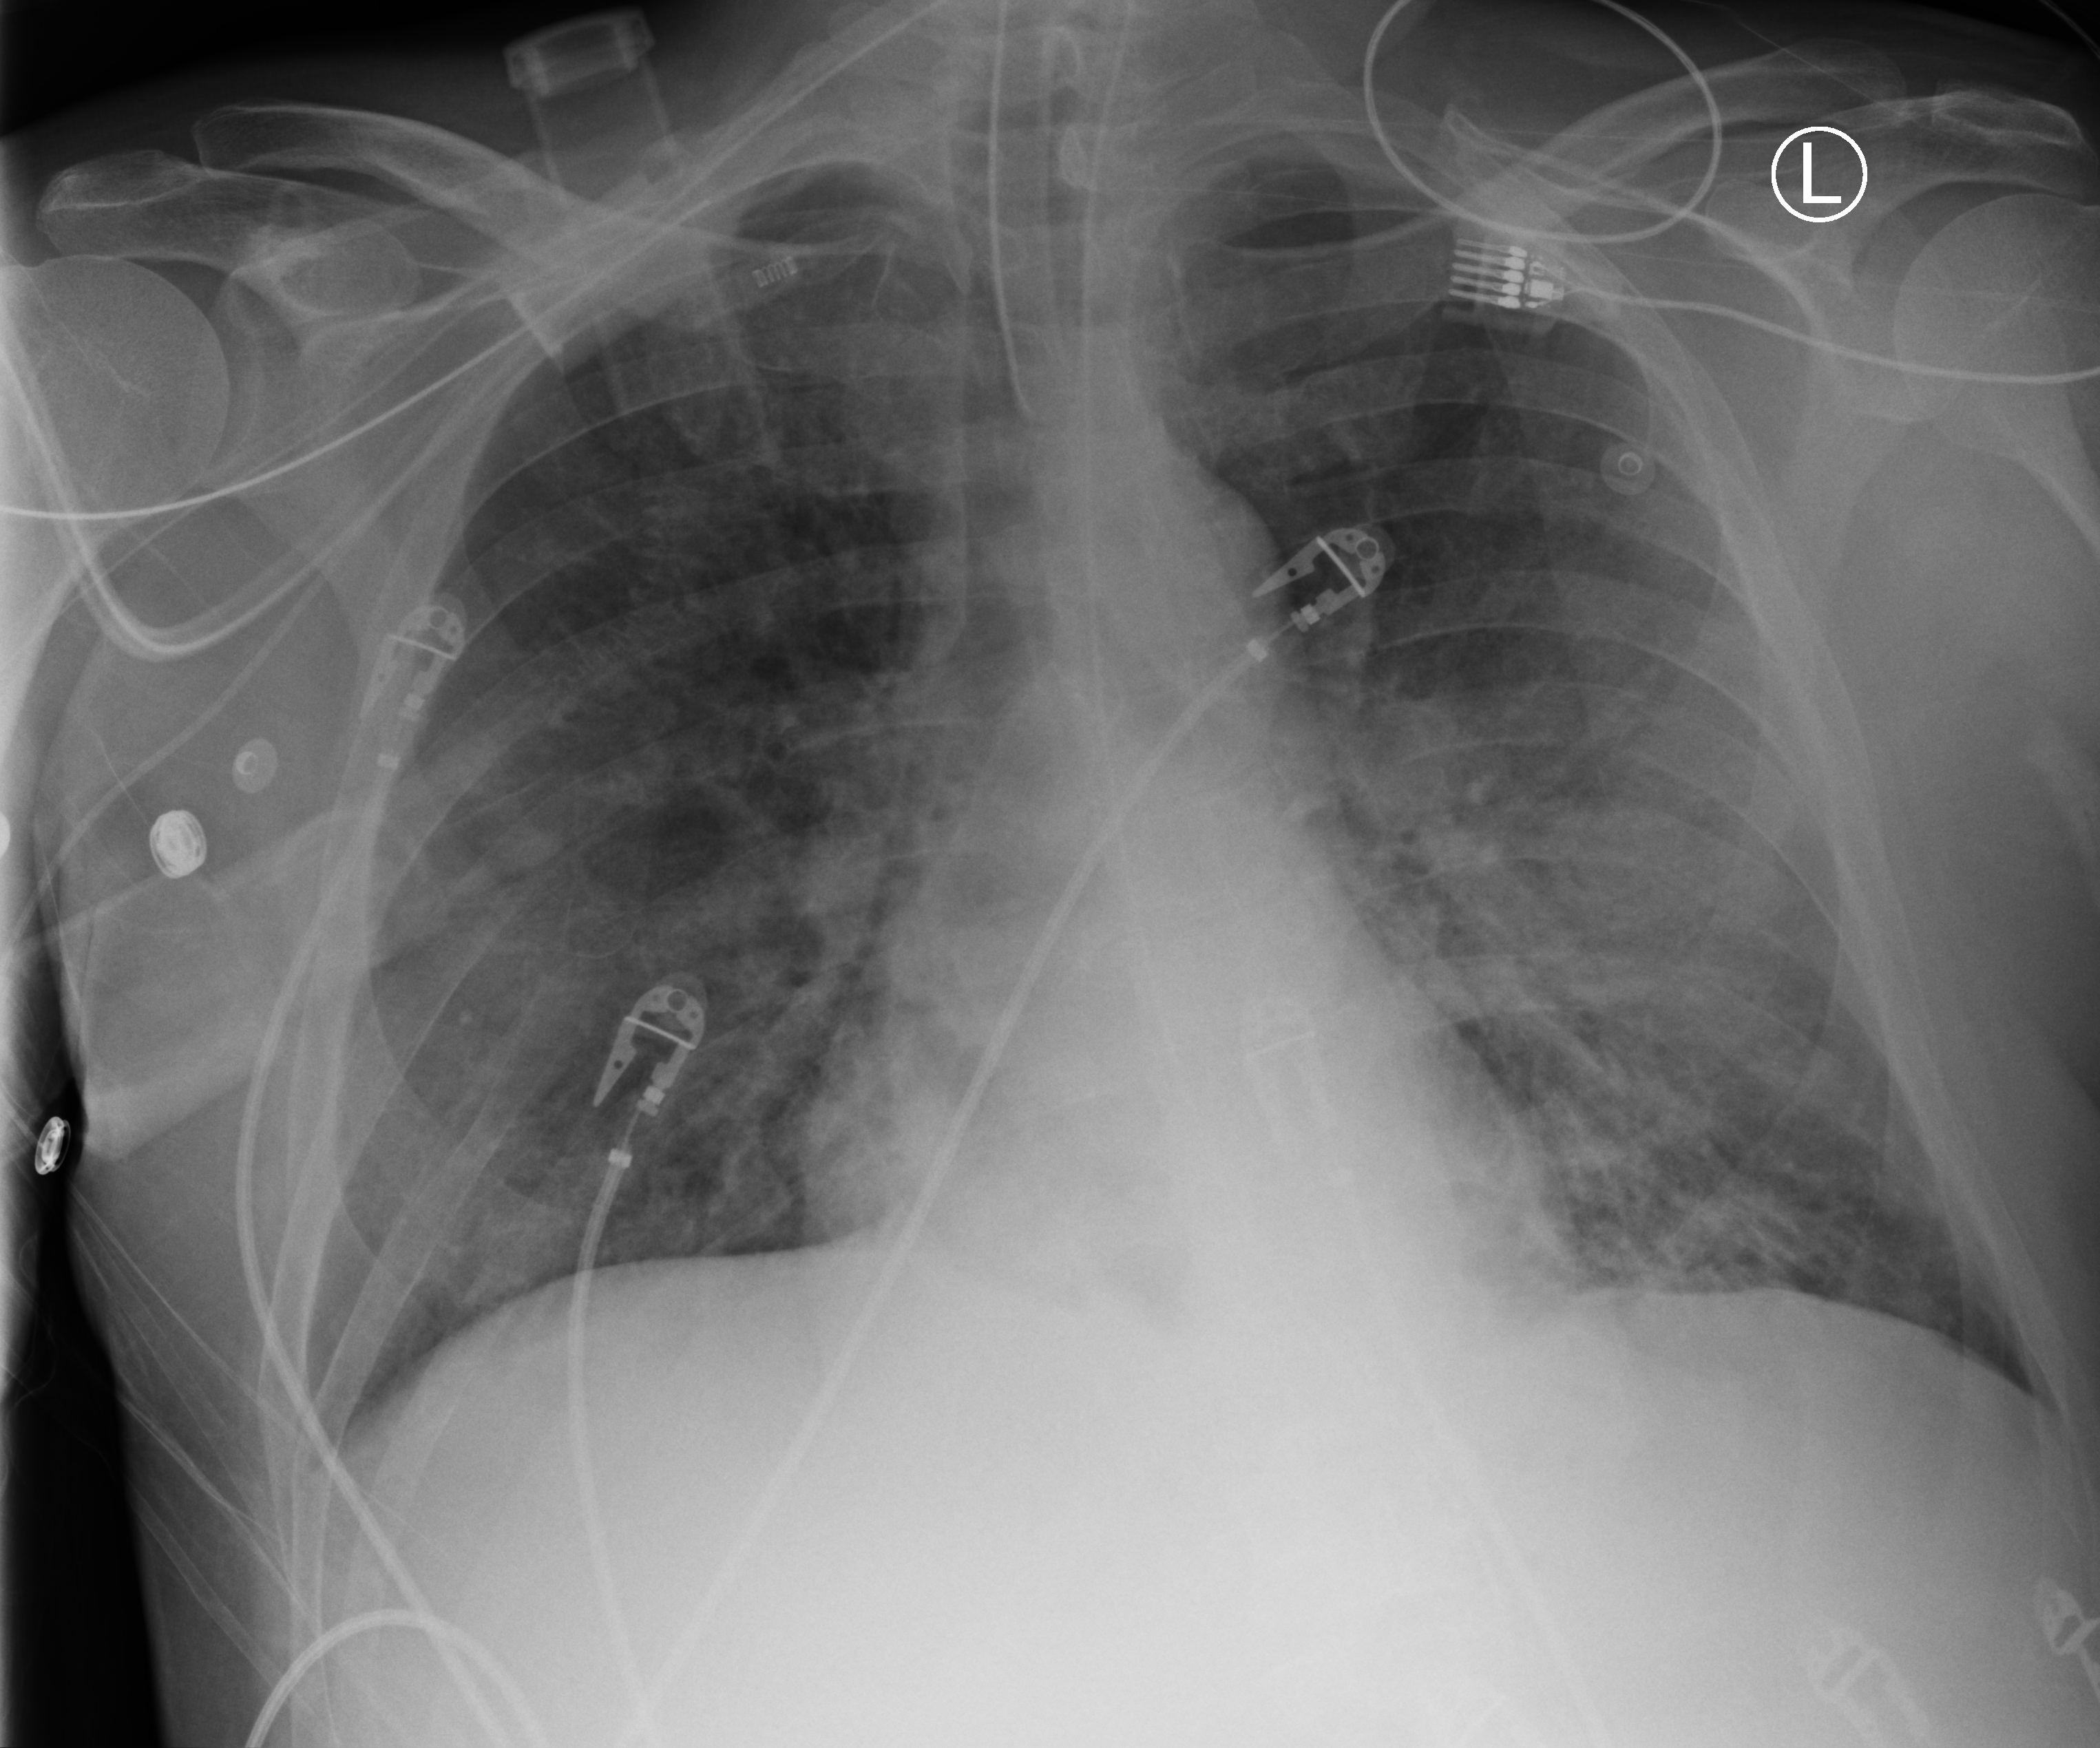
Portable chest radiograph. Patient hospitalised with COVID-19; male, aged 18–59 years.
From the hospital-stay record, not from the radiograph (when in the stay this image was taken is not recorded): admitted to intensive care during this hospital stay: yes.